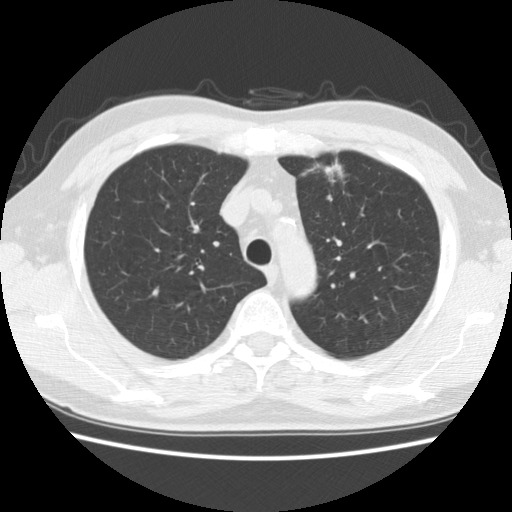
Low-dose screening chest CT, axial slice, second screening round (one year after baseline), lung window (W 1500 / L -600 HU), slice 43 of 172 in the series, 512 × 512 image matrix, field of view 337 × 337 mm. Male participant, aged 63 years at enrolment. Former smoker at enrolment.
Expert-annotated lung lesion, bounding box <298,147,358,204> (left, top, right, bottom; pixels). The exam's reader record, not a measurement of the box and not confirmed to be the same lesion: non-calcified nodule or mass ≥4 mm, left upper lobe, 23 × 18 mm, spiculated (stellate) margins, soft tissue attenuation, pre-existing on the prior screen: yes; interval growth: yes. Later outcome: lung cancer diagnosed 83 days after this screen — adenocarcinoma, NOS, left upper lobe, moderately differentiated (G2), stage IA (AJCC 6th edition), 14 mm at pathology.